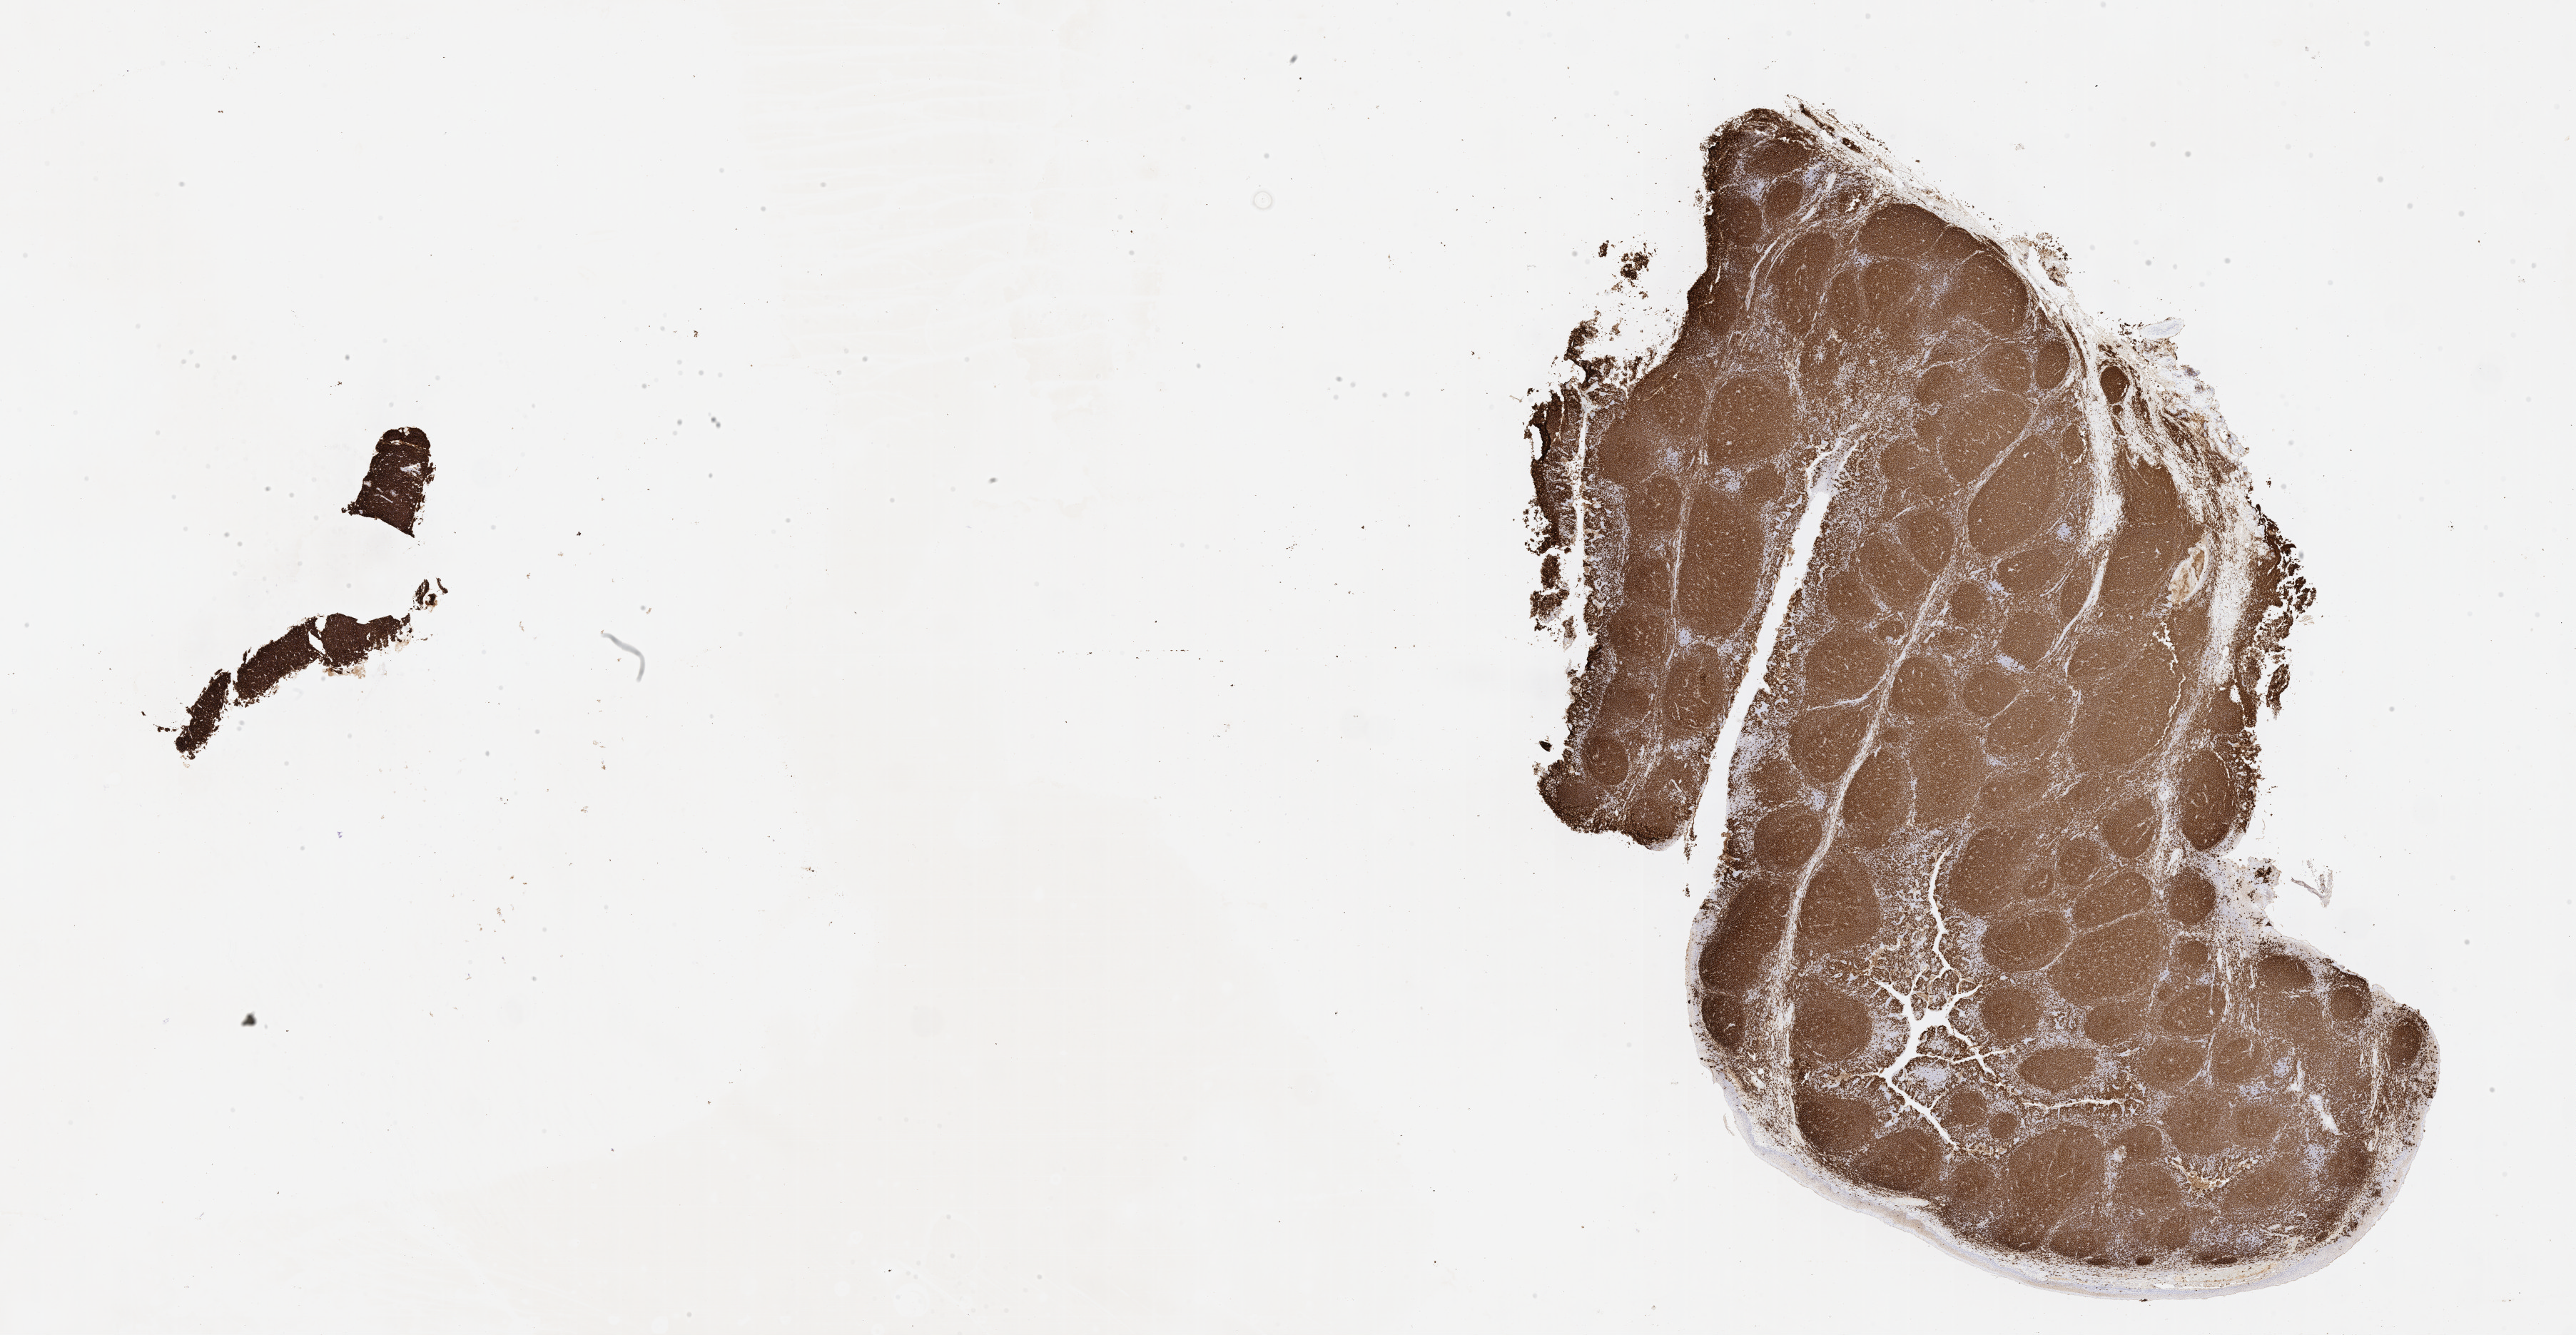
Immunohistochemistry (IHC) whole-slide image stained for CD20 — shown as a low-resolution overview of the whole scanned area (about 29.2 x 15.1 mm). Tumor tissue. Site: cranium. Male patient; age at initial diagnosis 6 years.
Diagnosis: Burkitt lymphoma, NOS.